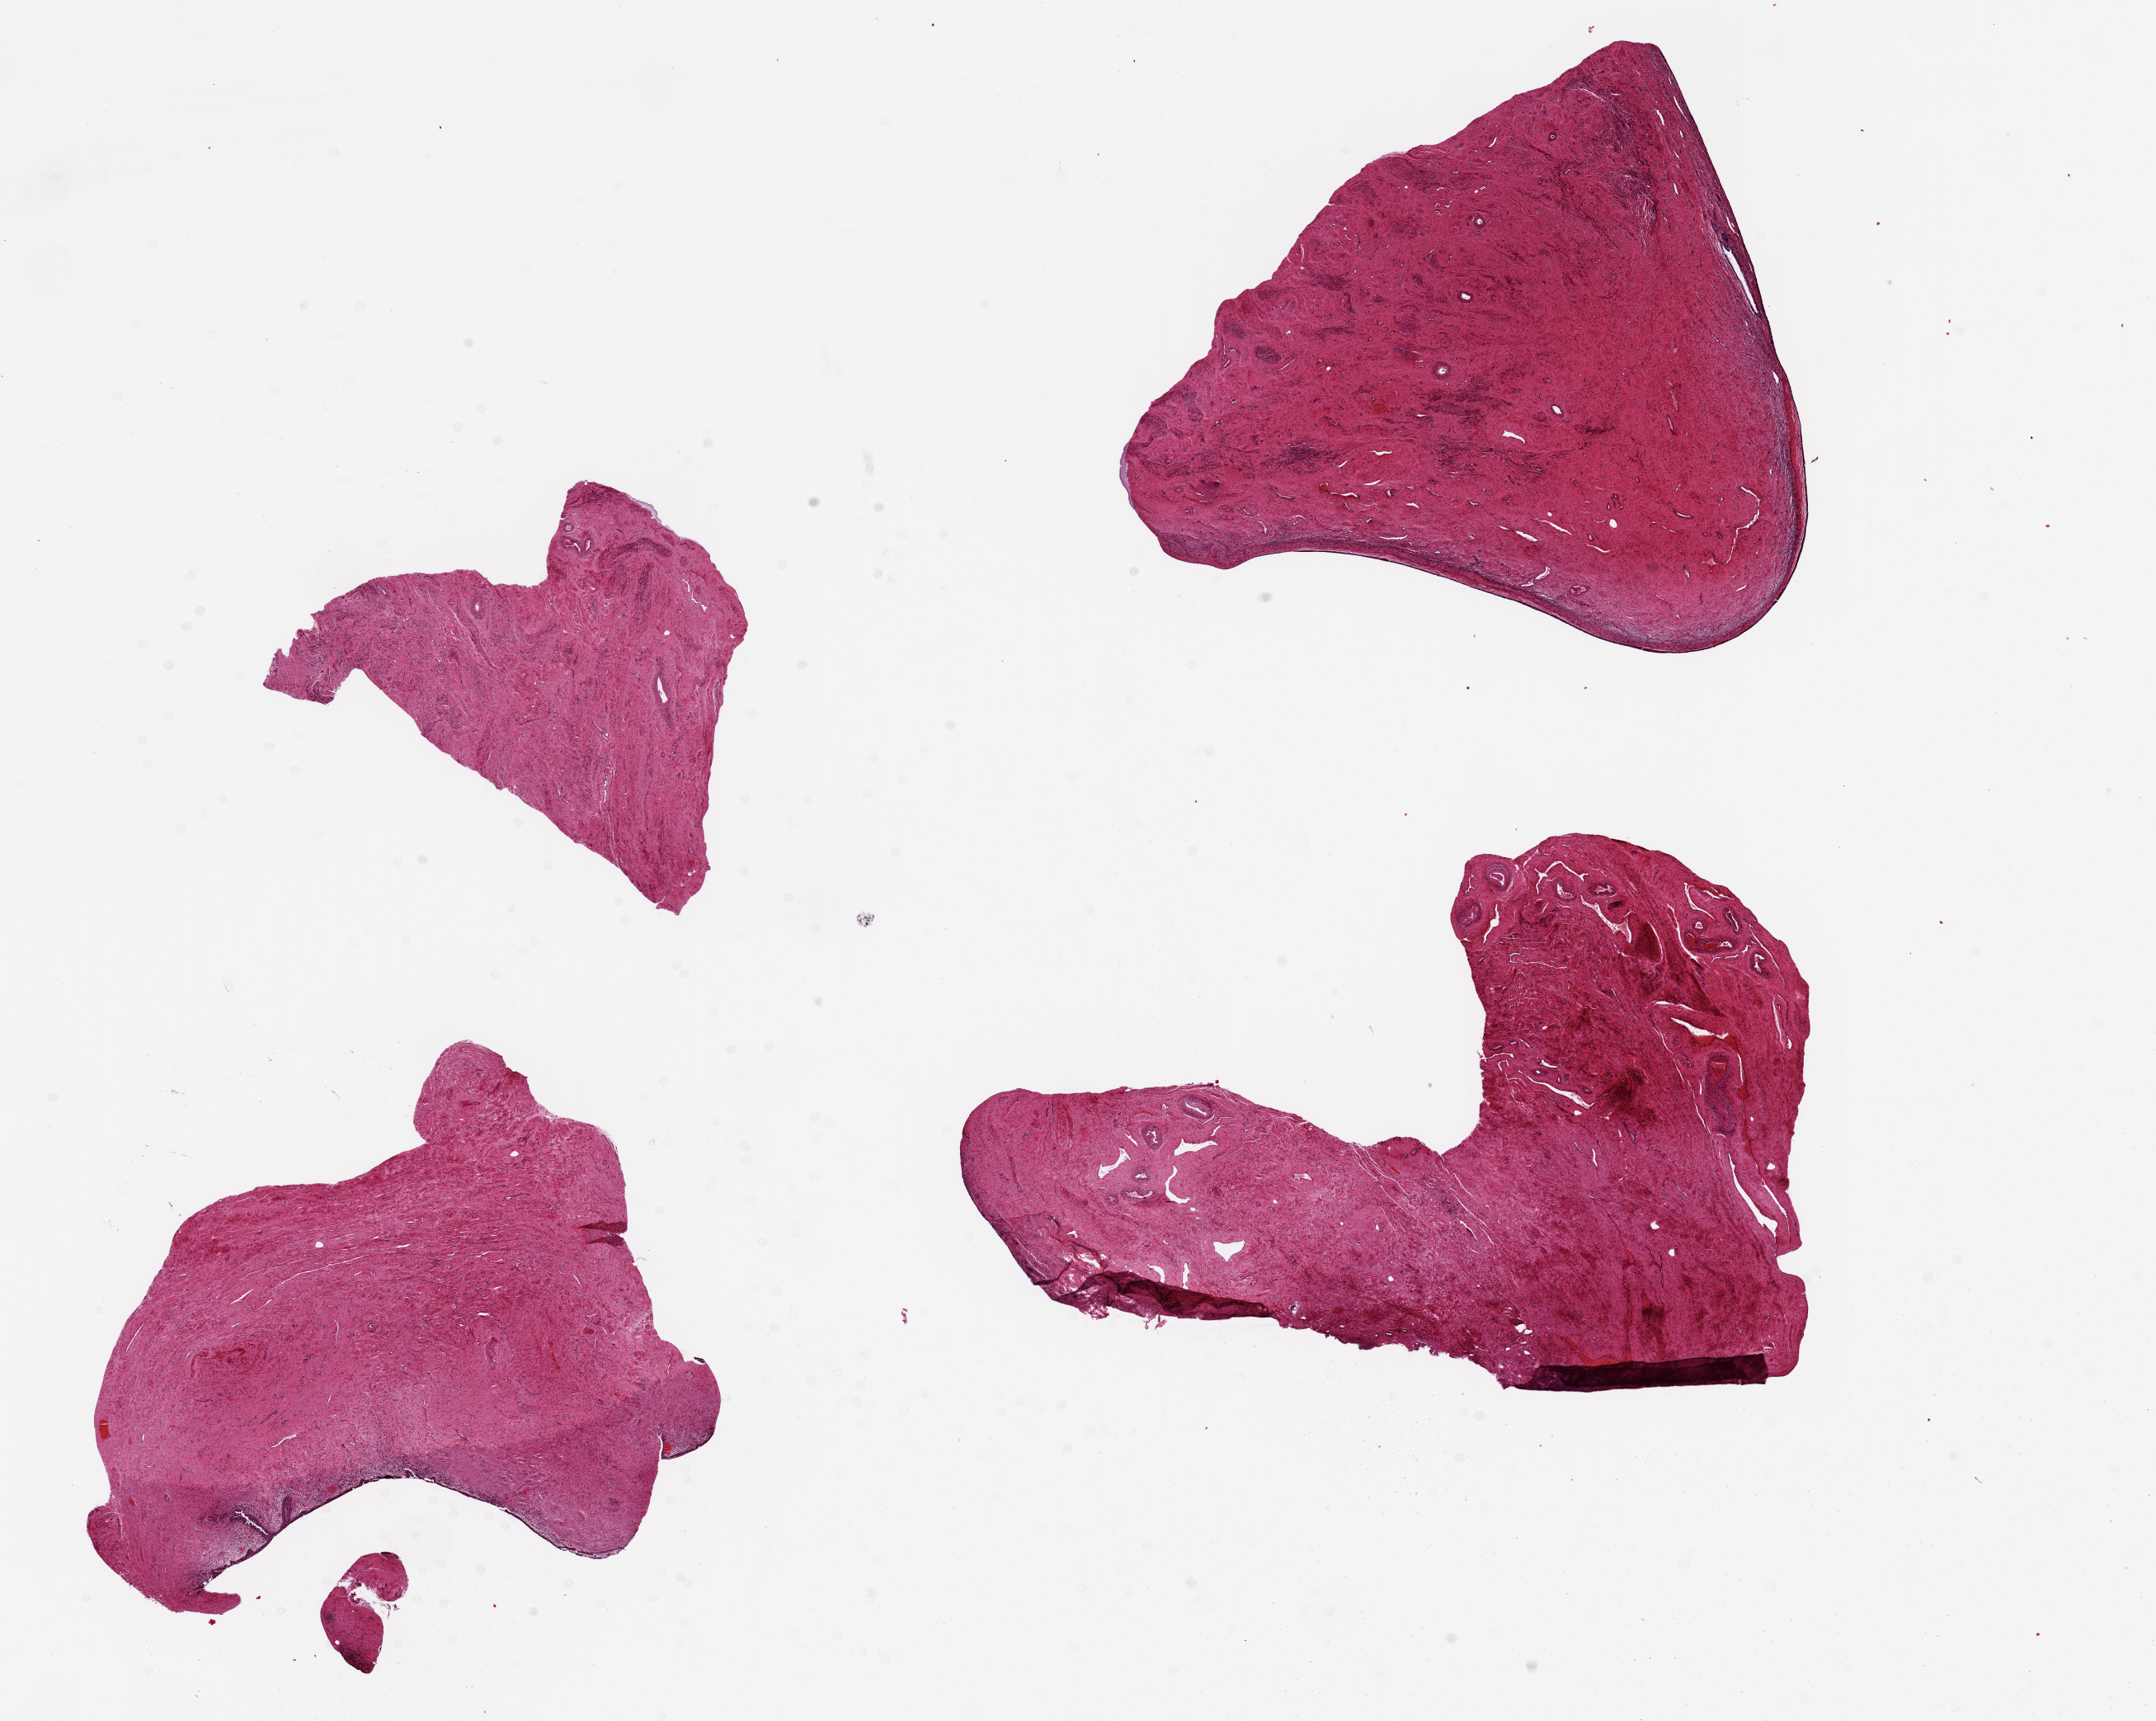
Whole-slide image, hematoxylin and eosin (H&E) stain — low-resolution overview of the scanned area, about 20.7 x 16.5 mm (slide scanned at 20x); PAXgene-fixed paraffin-embedded (PFPE) section; section of exocervix (target tissue); donor tissue sample. Donor: female.
Pathologist's review note for this sample: 4 pieces up to 8x5 mm; partially sloughed squamous lining on one piece, others do not have epithelium.